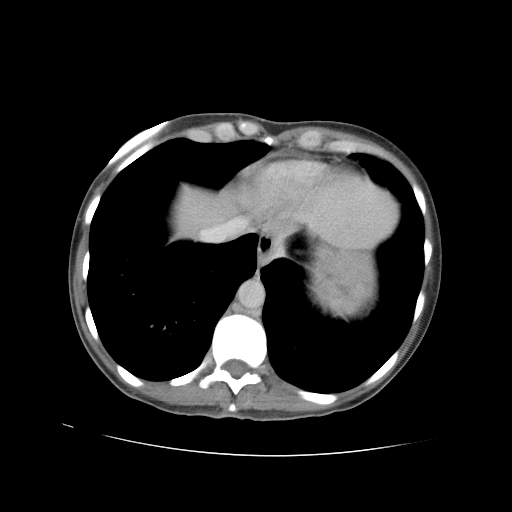
Contrast-enhanced abdominal CT, one axial slice. Slice 82 of 90 in the series (ordered by position). Reconstruction kernel STANDARD. Soft-tissue window (W 400 / L 40 HU). 5 mm slice thickness. 512 × 512 image matrix, field of view 360 × 360 mm. Female patient. Case-level facts recorded for this patient, not image findings: diagnosis: adrenocortical carcinoma; tumour side: left adrenal; tumour size at pathology: 18 cm; Ki-67 index: 11 %; stage (as recorded): 3.
Annotated regions visible in this slice (semi-automatic segmentation, software-assisted and operator-edited):
- mass: bounding box (x1, y1, x2, y2) in pixels: (315, 248, 371, 312)